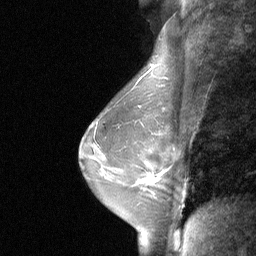
Breast MRI (dynamic contrast-enhanced), one sagittal slice; slice 44 of 64 in the series (ordered by position); dynamic contrast-enhanced study with each time point stored as its own series, time point 2 of 3 at this slice position (early post-contrast, ordered by acquisition time); 1.5 T; TE 4.8 ms, TR 27 ms; 2 mm slice thickness; 256 × 256 image matrix, field of view 200 × 200 mm. Patient: female, 48 years. From the clinical record (not read from this slice): setting: breast cancer imaged before/during neoadjuvant chemotherapy; receptor status: HR-positive, HER2-negative.
Annotated regions visible in this slice (semi-automatic segmentation, software-assisted and operator-edited):
- analysis volume of interest (the breast-tissue region the enhancement analysis was run in; not a lesion): bounding box <131,165,170,200> (left, top, right, bottom; pixels)
- tumour enhancement mask (voxels above the 90 % enhancement threshold inside the analysis volume of interest): <147,175,158,183>